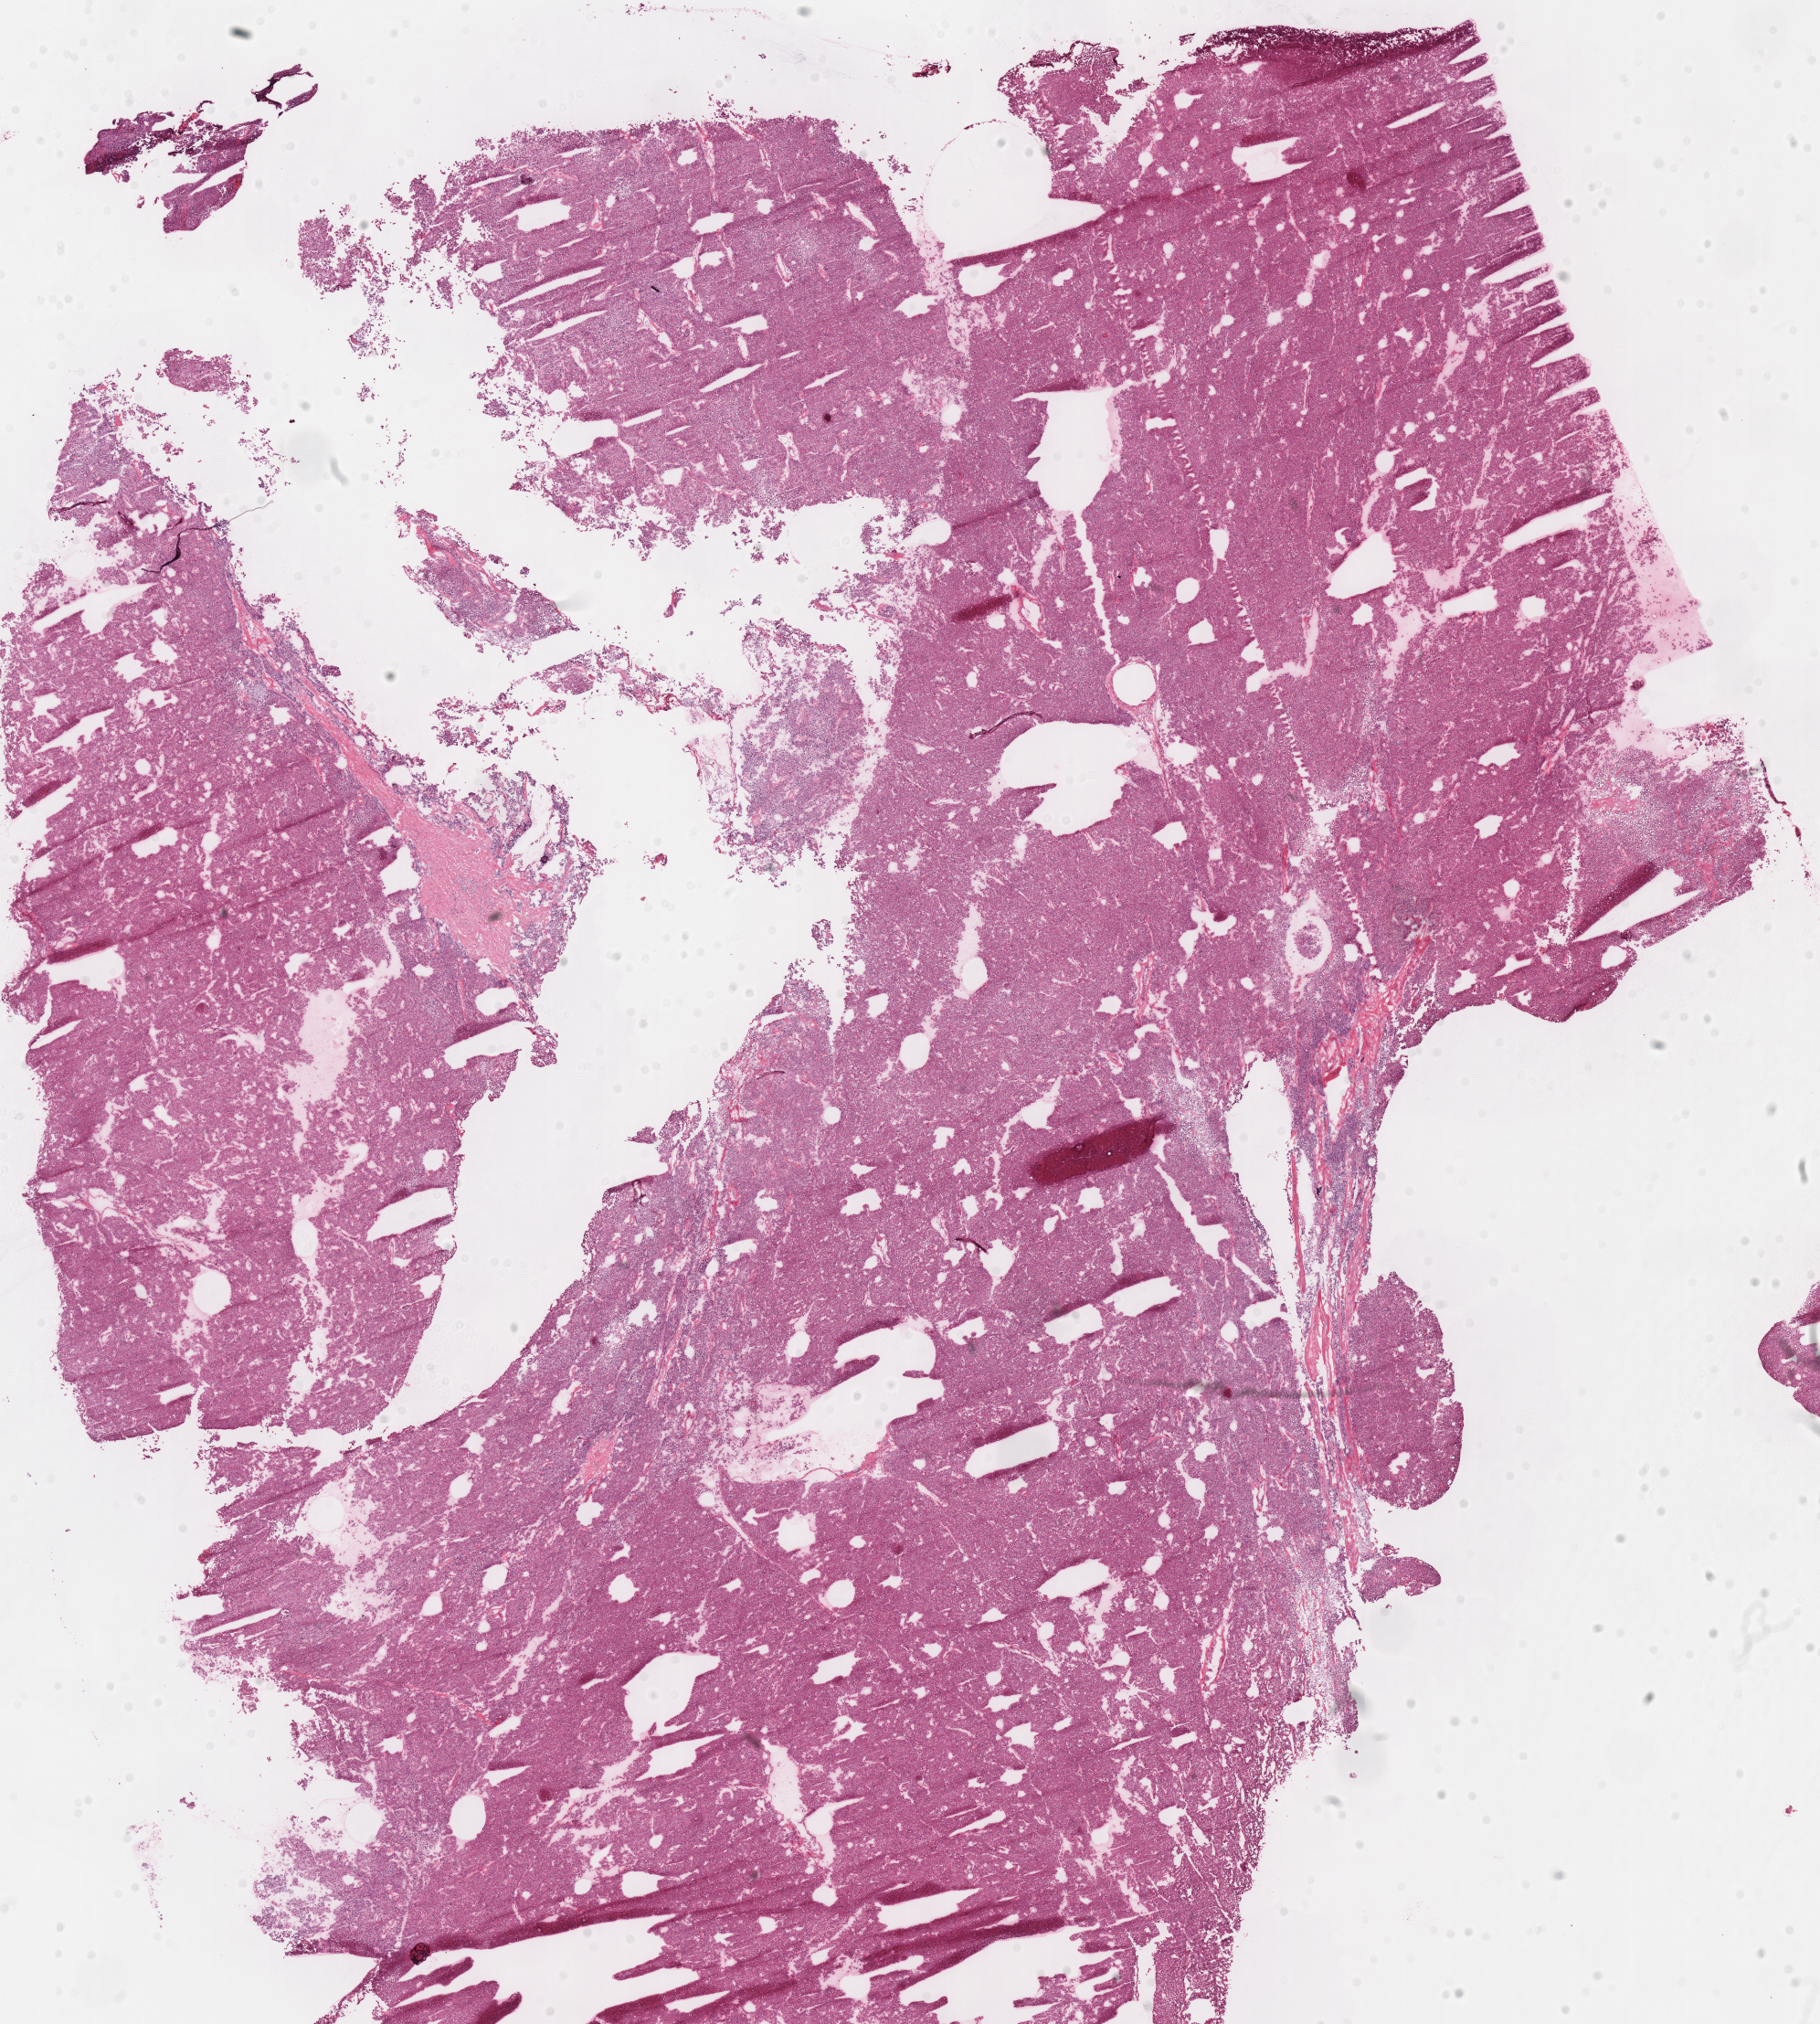
Digitized Hematoxylin and eosin (H&E) stained tissue section (whole slide), low-resolution overview of the scanned area, about 15.7 x 17.4 mm (slide scanned at 40x), frozen section from the top of the tissue portion, primary tumour sample from the kidney. Patient: male, age at initial diagnosis 60 years. Composition of this section per pathologist review: tumour cells 98%, tumour nuclei 90%, normal cells 0%, stromal cells 0%, necrosis 2%. Infiltration values recorded for this section: lymphocyte infiltration 1%, monocyte infiltration 0%, neutrophil infiltration 0%.
Pathologic diagnosis: Renal cell carcinoma, chromophobe type. Lymph nodes positive (case pathology): 0 of 4 examined. AJCC pathologic stage: II (6th edition). Laterality: left. TNM: T2b N0 M0.